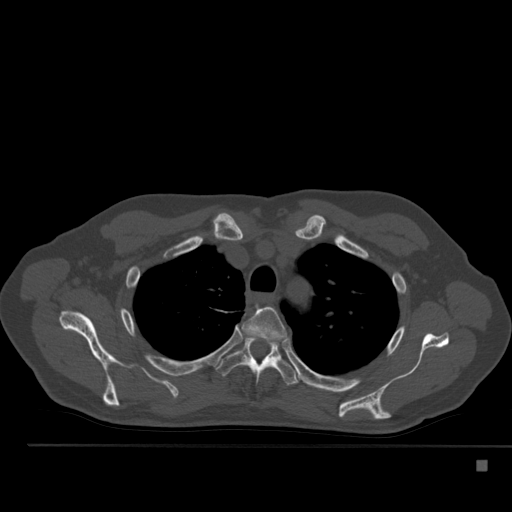
CT including the spine, one axial slice. Slice 388 of 517 in the series (ordered by position). Reconstruction kernel Br40s. Bone window (W 1800 / L 400 HU). 1.5 mm slice thickness. 512 × 512 image matrix, field of view 408 × 408 mm. Patient: male, 70 years. From the clinical record (not read from this slice): primary cancer: renal.
Structures marked on this image (semi-automatic segmentation, software-assisted and operator-edited):
- T3 vertebra: bounding box <242,307,287,343> (left, top, right, bottom; pixels)
- T4 vertebra: <216,337,301,385>